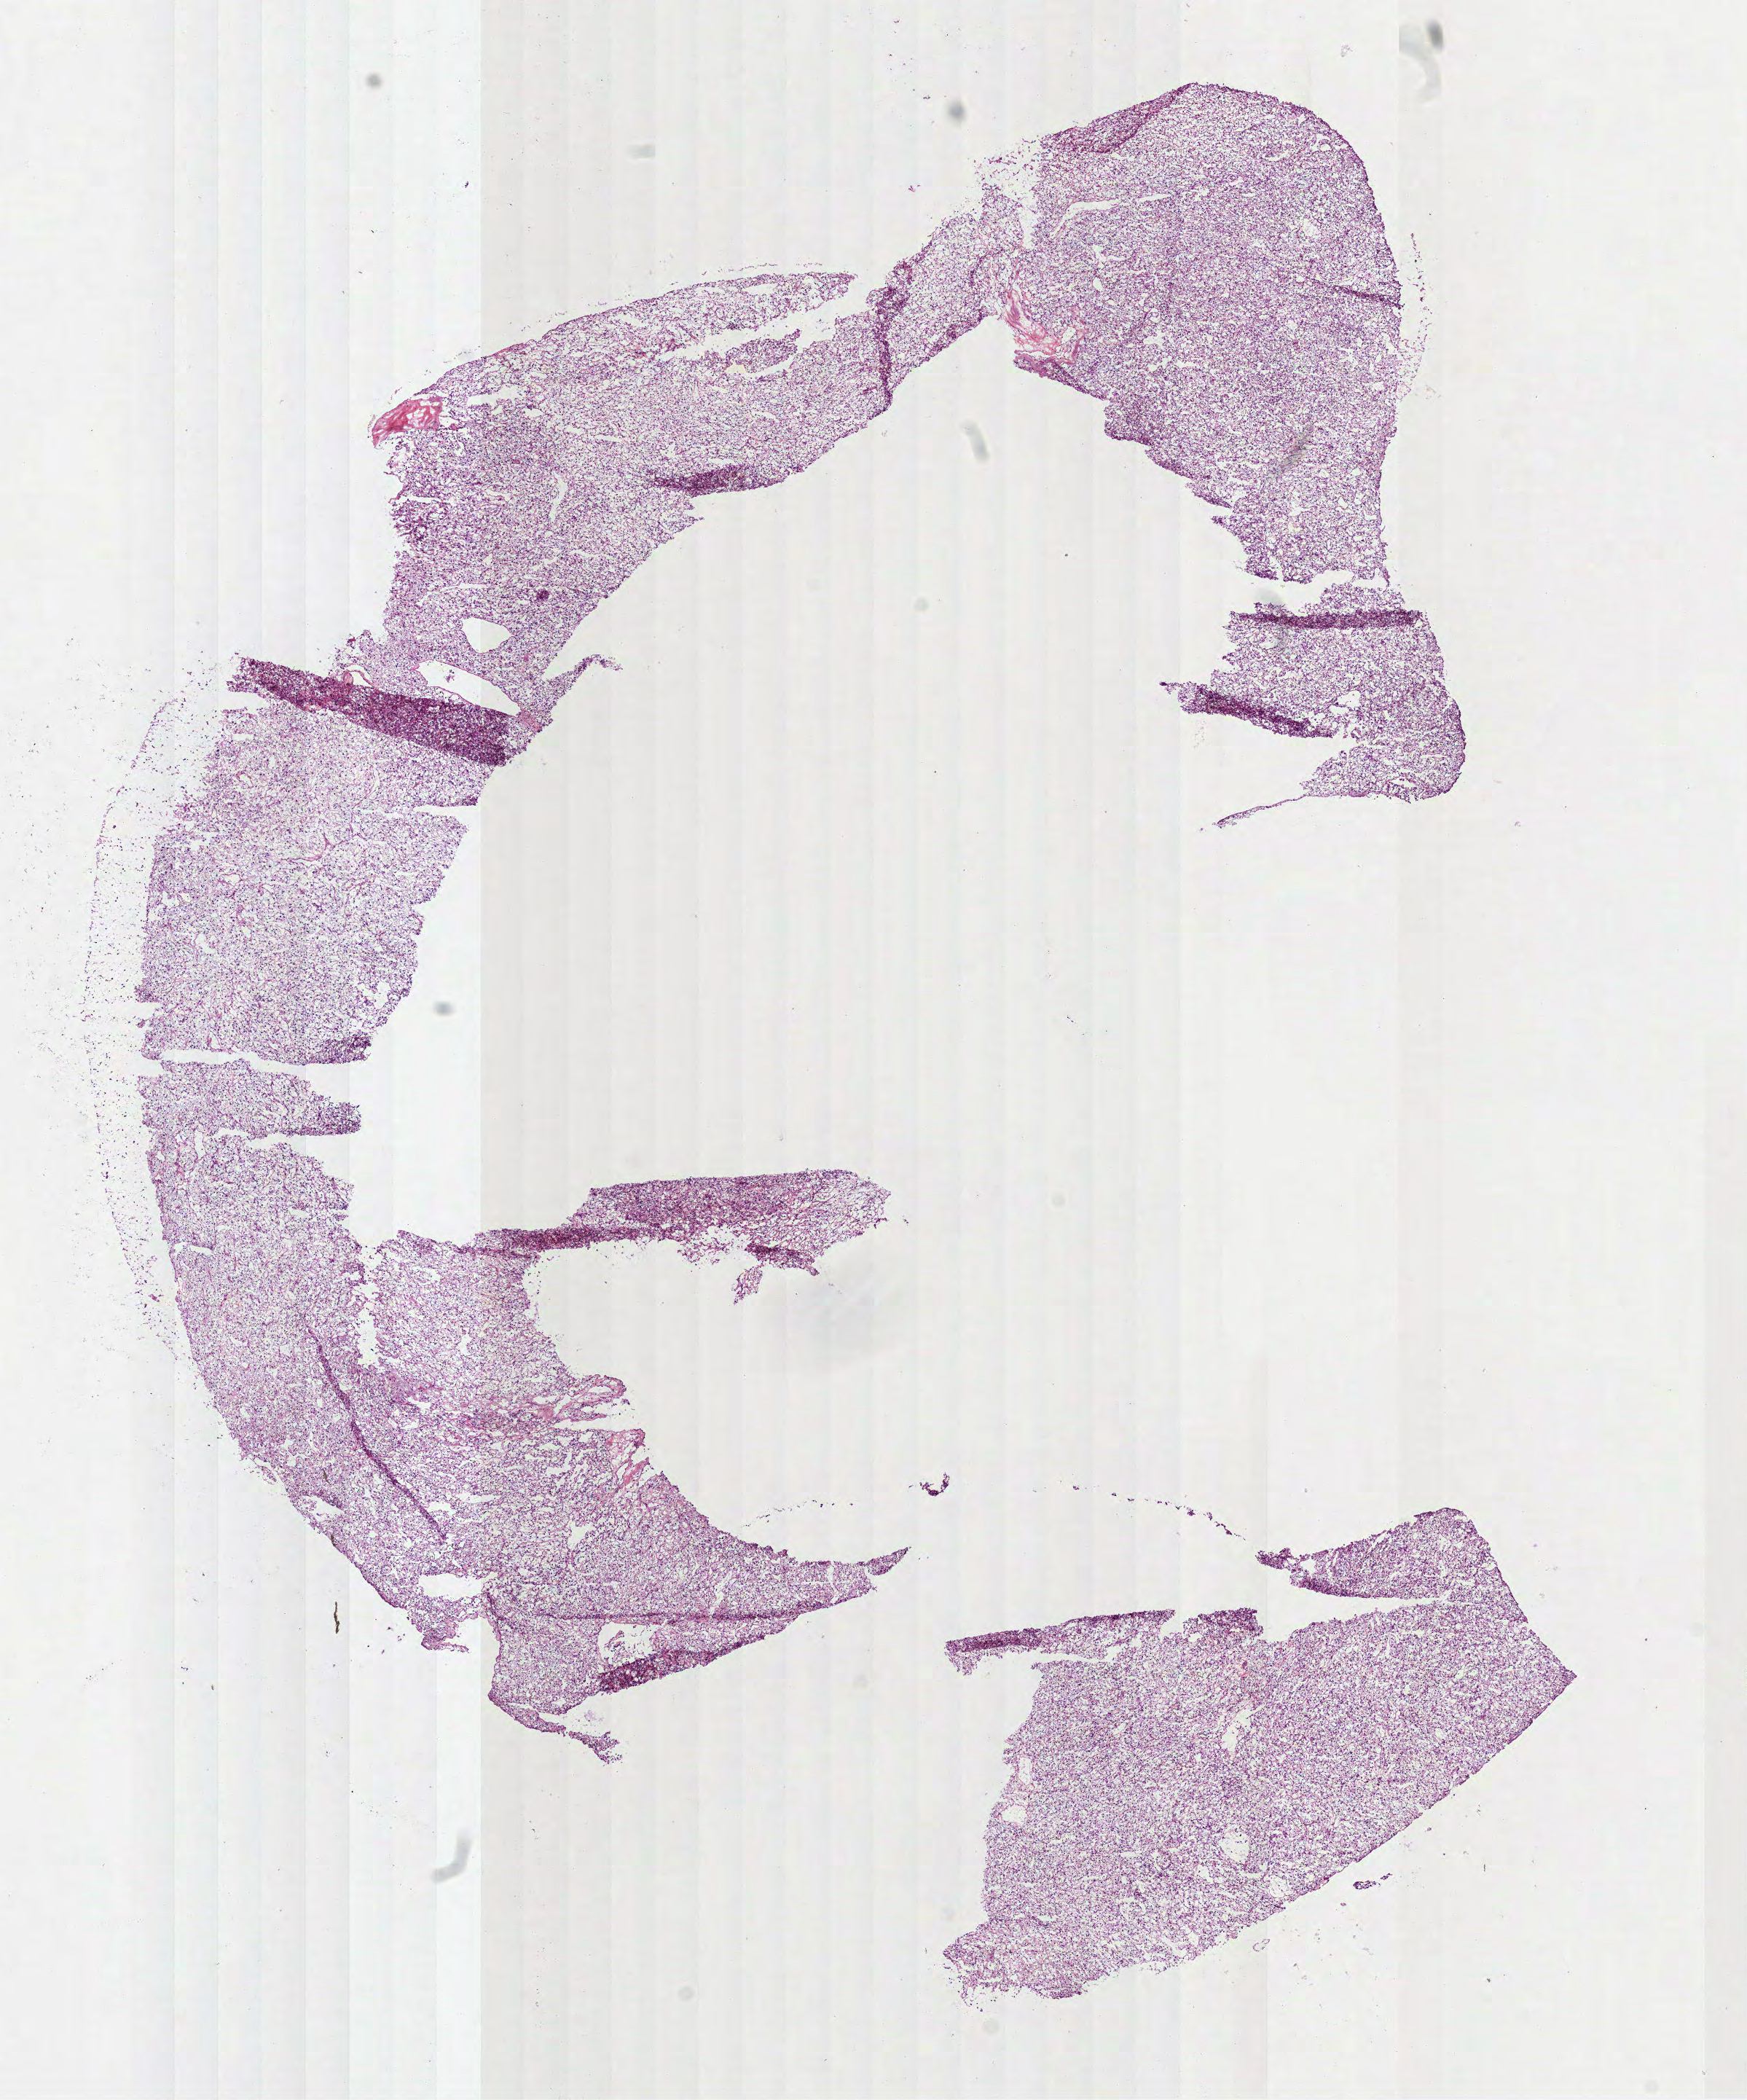
H&E-stained whole-slide image — a low-resolution overview of the entire scanned area, about 9.7 x 11.6 mm. Frozen section. Sample: primary tumour, kidney. Male patient; age at initial diagnosis 74 years. Histologic grade: G3 (poorly differentiated). Composition of this section per pathologist review: tumour cells 95%, tumour nuclei 85%, normal cells 0%, stromal cells 5%, necrosis 0%.
Laterality: left. TNM: T3a NX M0. Pathologic diagnosis: Clear cell adenocarcinoma, NOS. AJCC pathologic stage: III.